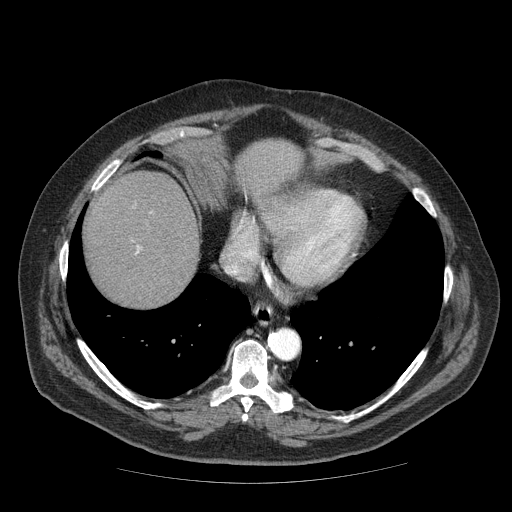
Contrast-enhanced abdominal CT (liver protocol), one axial slice; slice 64 of 85 in the series (ordered by position); reconstruction kernel STANDARD; 120 kVp; soft-tissue window (W 400 / L 40 HU); 2.5 mm slice thickness; 512 × 512 image matrix. Case-level facts recorded for this patient, not image findings: diagnosis: hepatocellular carcinoma (patient treated with transarterial chemoembolisation; whether this scan precedes or follows treatment is not stated here); TNM stage (as recorded): Stage-IIIA; Child-Pugh class: A.
Outlined on this slice (semi-automatic segmentation, software-assisted and operator-edited):
- liver parenchyma outside the tumour (the mass and vessels are separate outlines, so this box may not span the whole liver): box from (x=84, y=142) to (x=300, y=306) px